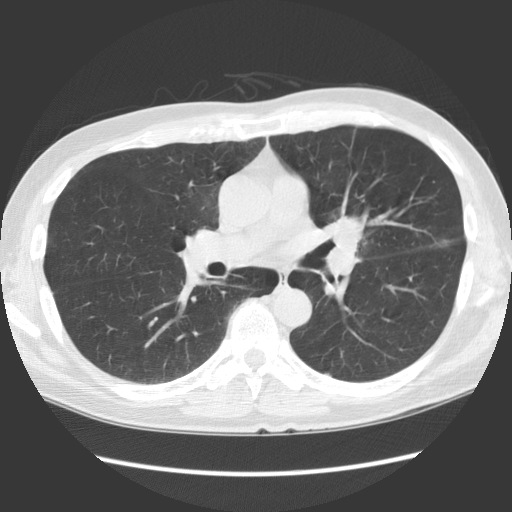
Axial slice from a low-dose chest CT screening exam, baseline annual screen, lung window (W 1500 / L -600 HU), 2.5 mm slice thickness, standard (soft-tissue) reconstruction kernel (STANDARD), 512 × 512 image matrix. Male participant, aged 61 years at enrolment.
• Expert-annotated lung lesion, bounding box [x1, y1, x2, y2] px = [291, 197, 390, 298].
• Screening reader's record for this exam (one nodule recorded; not confirmed to be the boxed lesion): non-calcified nodule or mass ≥4 mm, lingula, 35 × 35 mm, spiculated (stellate) margins, soft tissue attenuation.
• Official screen result: positive, change unspecified: nodule(s) >= 4 mm or enlarging nodule(s), mass(es), or other non-specific abnormalities suspicious for lung cancer.
• Later outcome: lung cancer diagnosed 58 days after this screen — squamous cell carcinoma, NOS, left hilum, left main stem bronchus, poorly differentiated (G3), stage IA (AJCC 6th edition), 40 mm at pathology.